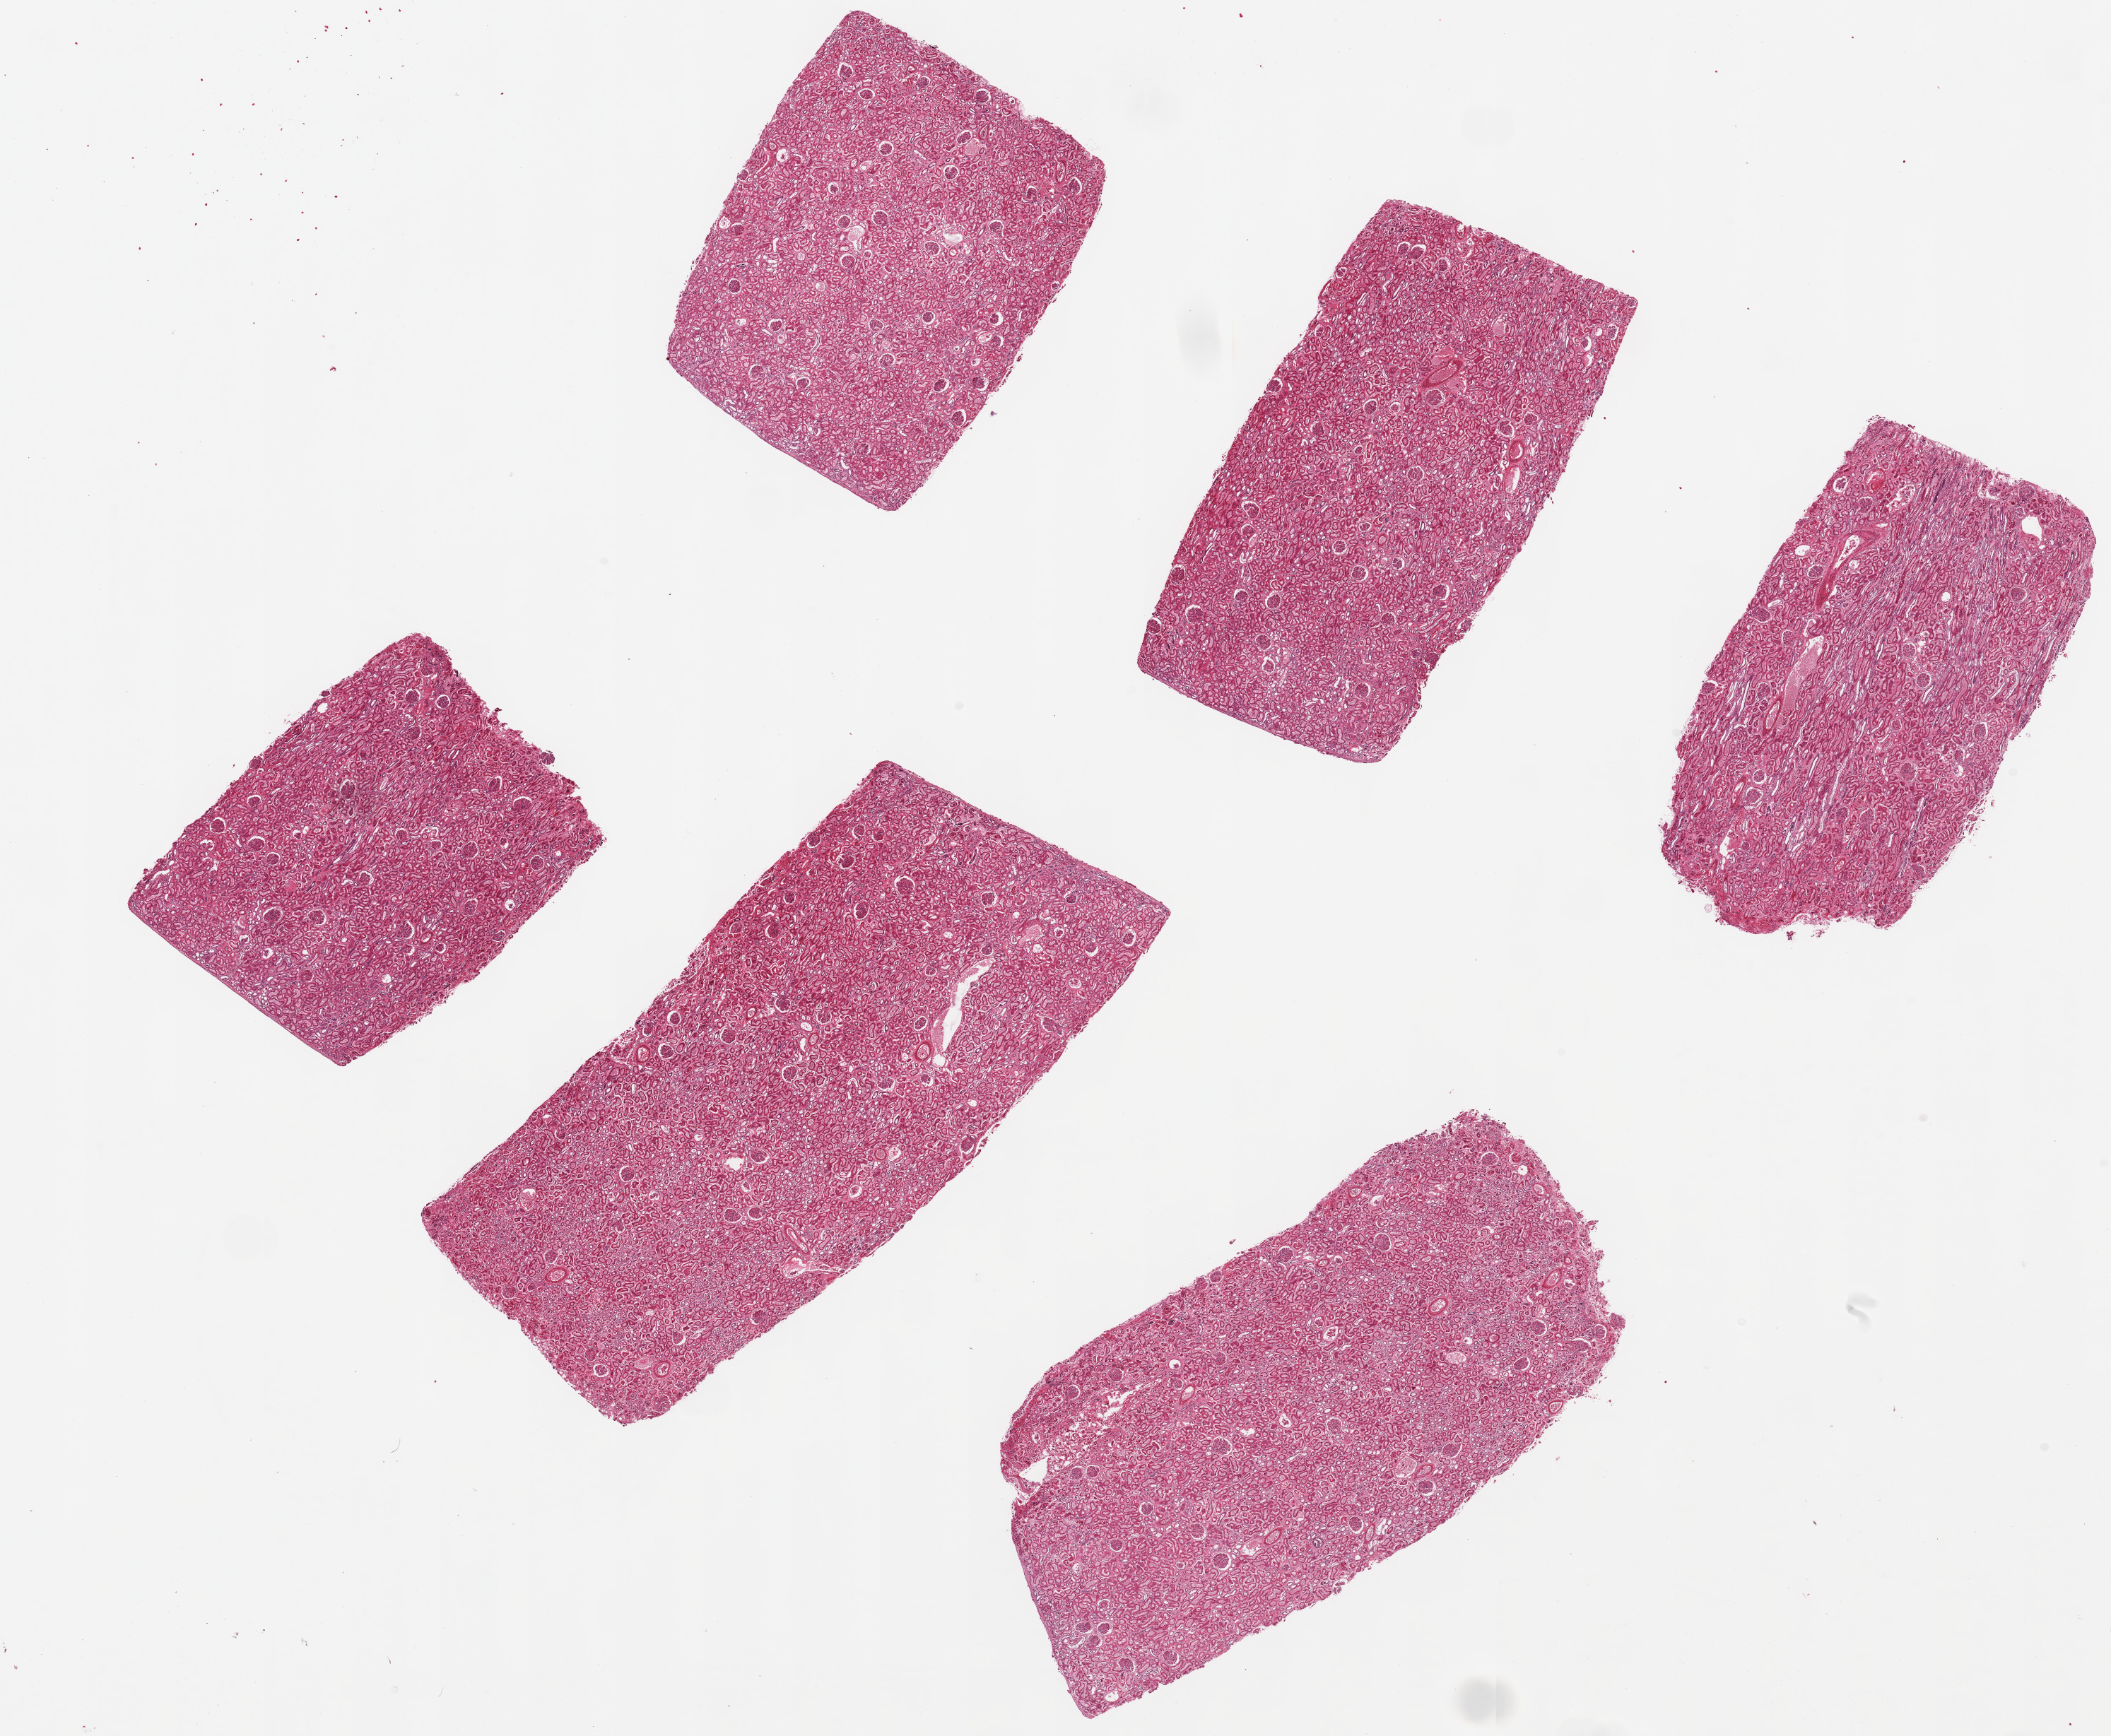
H&E whole-slide image — whole scanned area (about 23.6 x 19.4 mm, acquisition: 20x scan) shown as a low-resolution overview; PAXgene-fixed paraffin-embedded (PFPE) section; sampled site (target tissue): renal cortex; tissue donor sample. Female donor.
Review note (as recorded): 6 ~6.5x3.5mm pieces. Tubules more autolyzed than glomeruli.